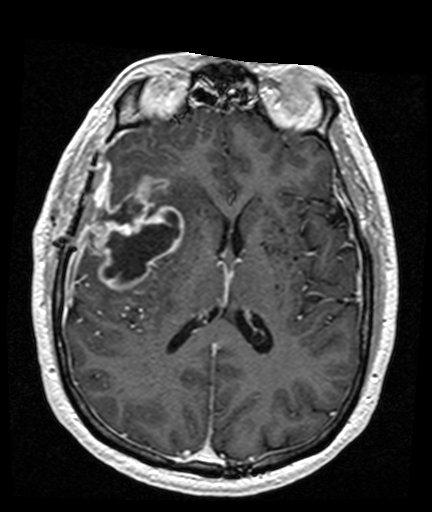
Brain MRI from a brain-tumour surgery series, one axial slice; position 76 of 176 along the scan axis; T1-weighted post-contrast; 1 mm slice thickness; 432 × 512 image matrix, field of view 194 × 230 mm. From the clinical record (not read from this slice): histopathology: Glioblastoma; WHO grade: 4; IDH mutation: no; tumour location: Right Frontal Temporal, Posterior Sylvian Fissure.
Annotated regions visible in this slice (manually delineated by an expert):
- tumour: box from (x=91, y=176) to (x=183, y=292) px